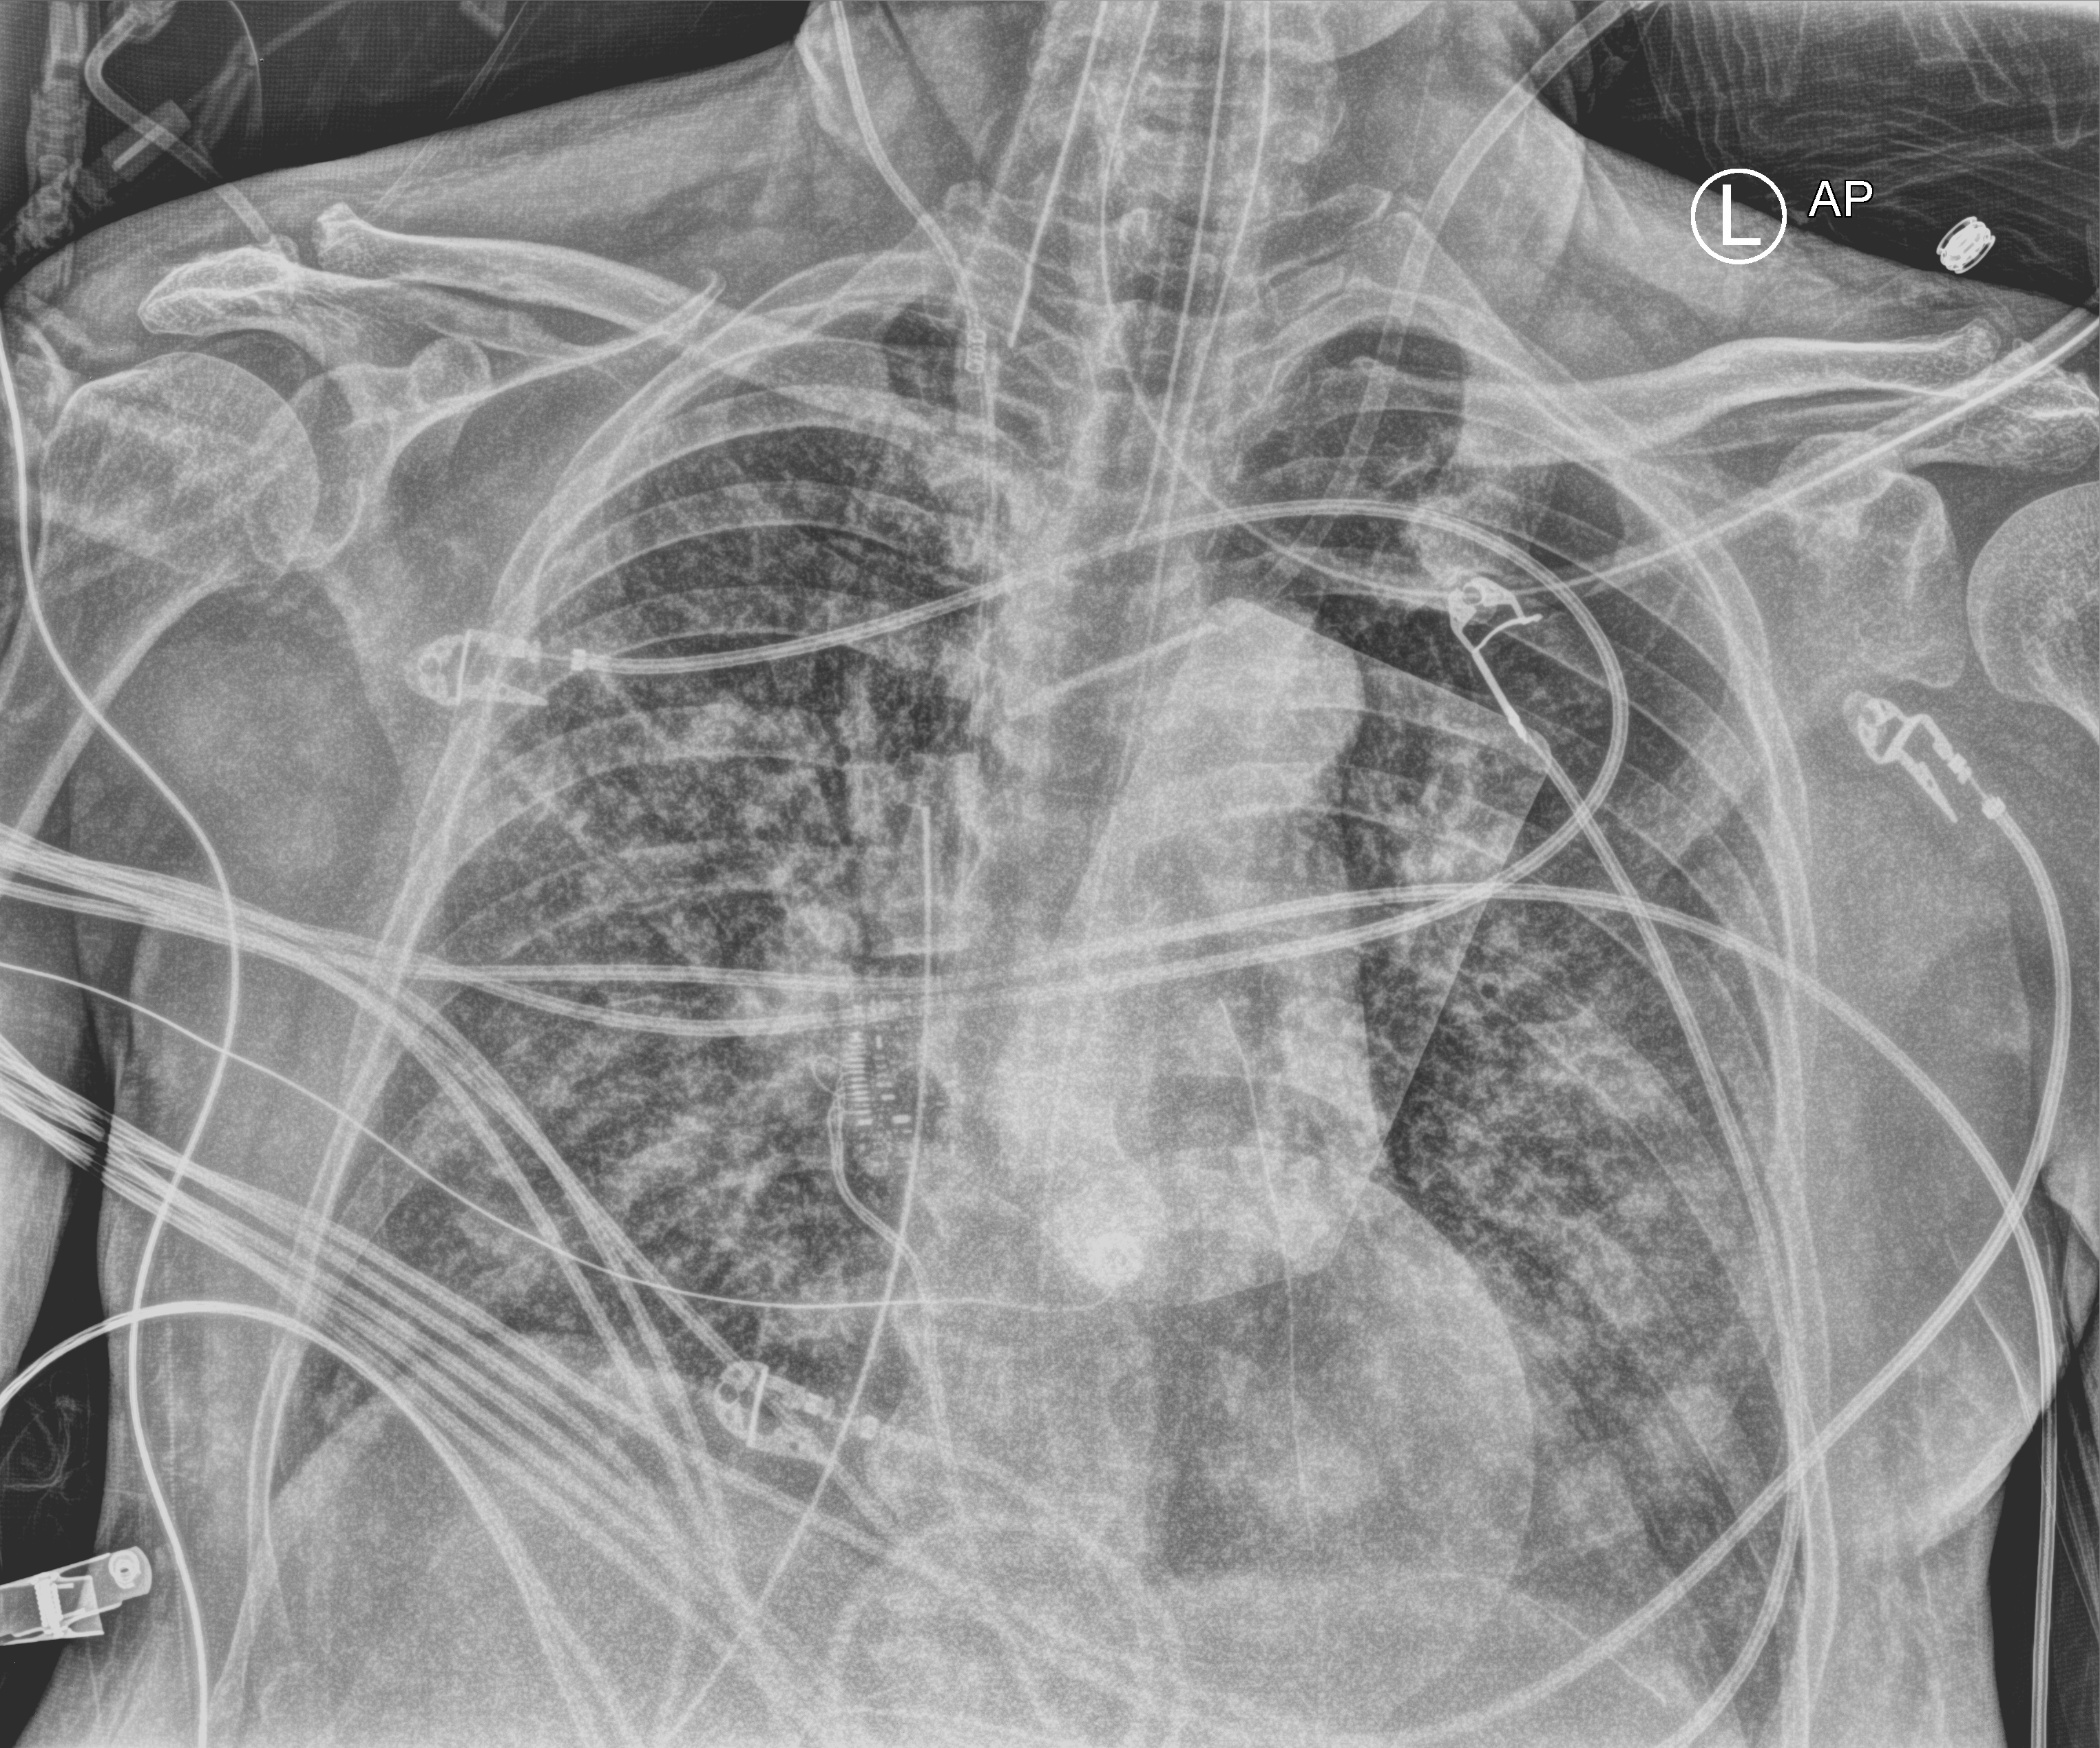
Portable chest radiograph, anteroposterior (AP) projection. Male patient hospitalised with COVID-19, age 60–74 years.
Hospital-stay facts (about this admission, not read from this image; timing relative to this image not recorded): length of hospital stay: 26 days.